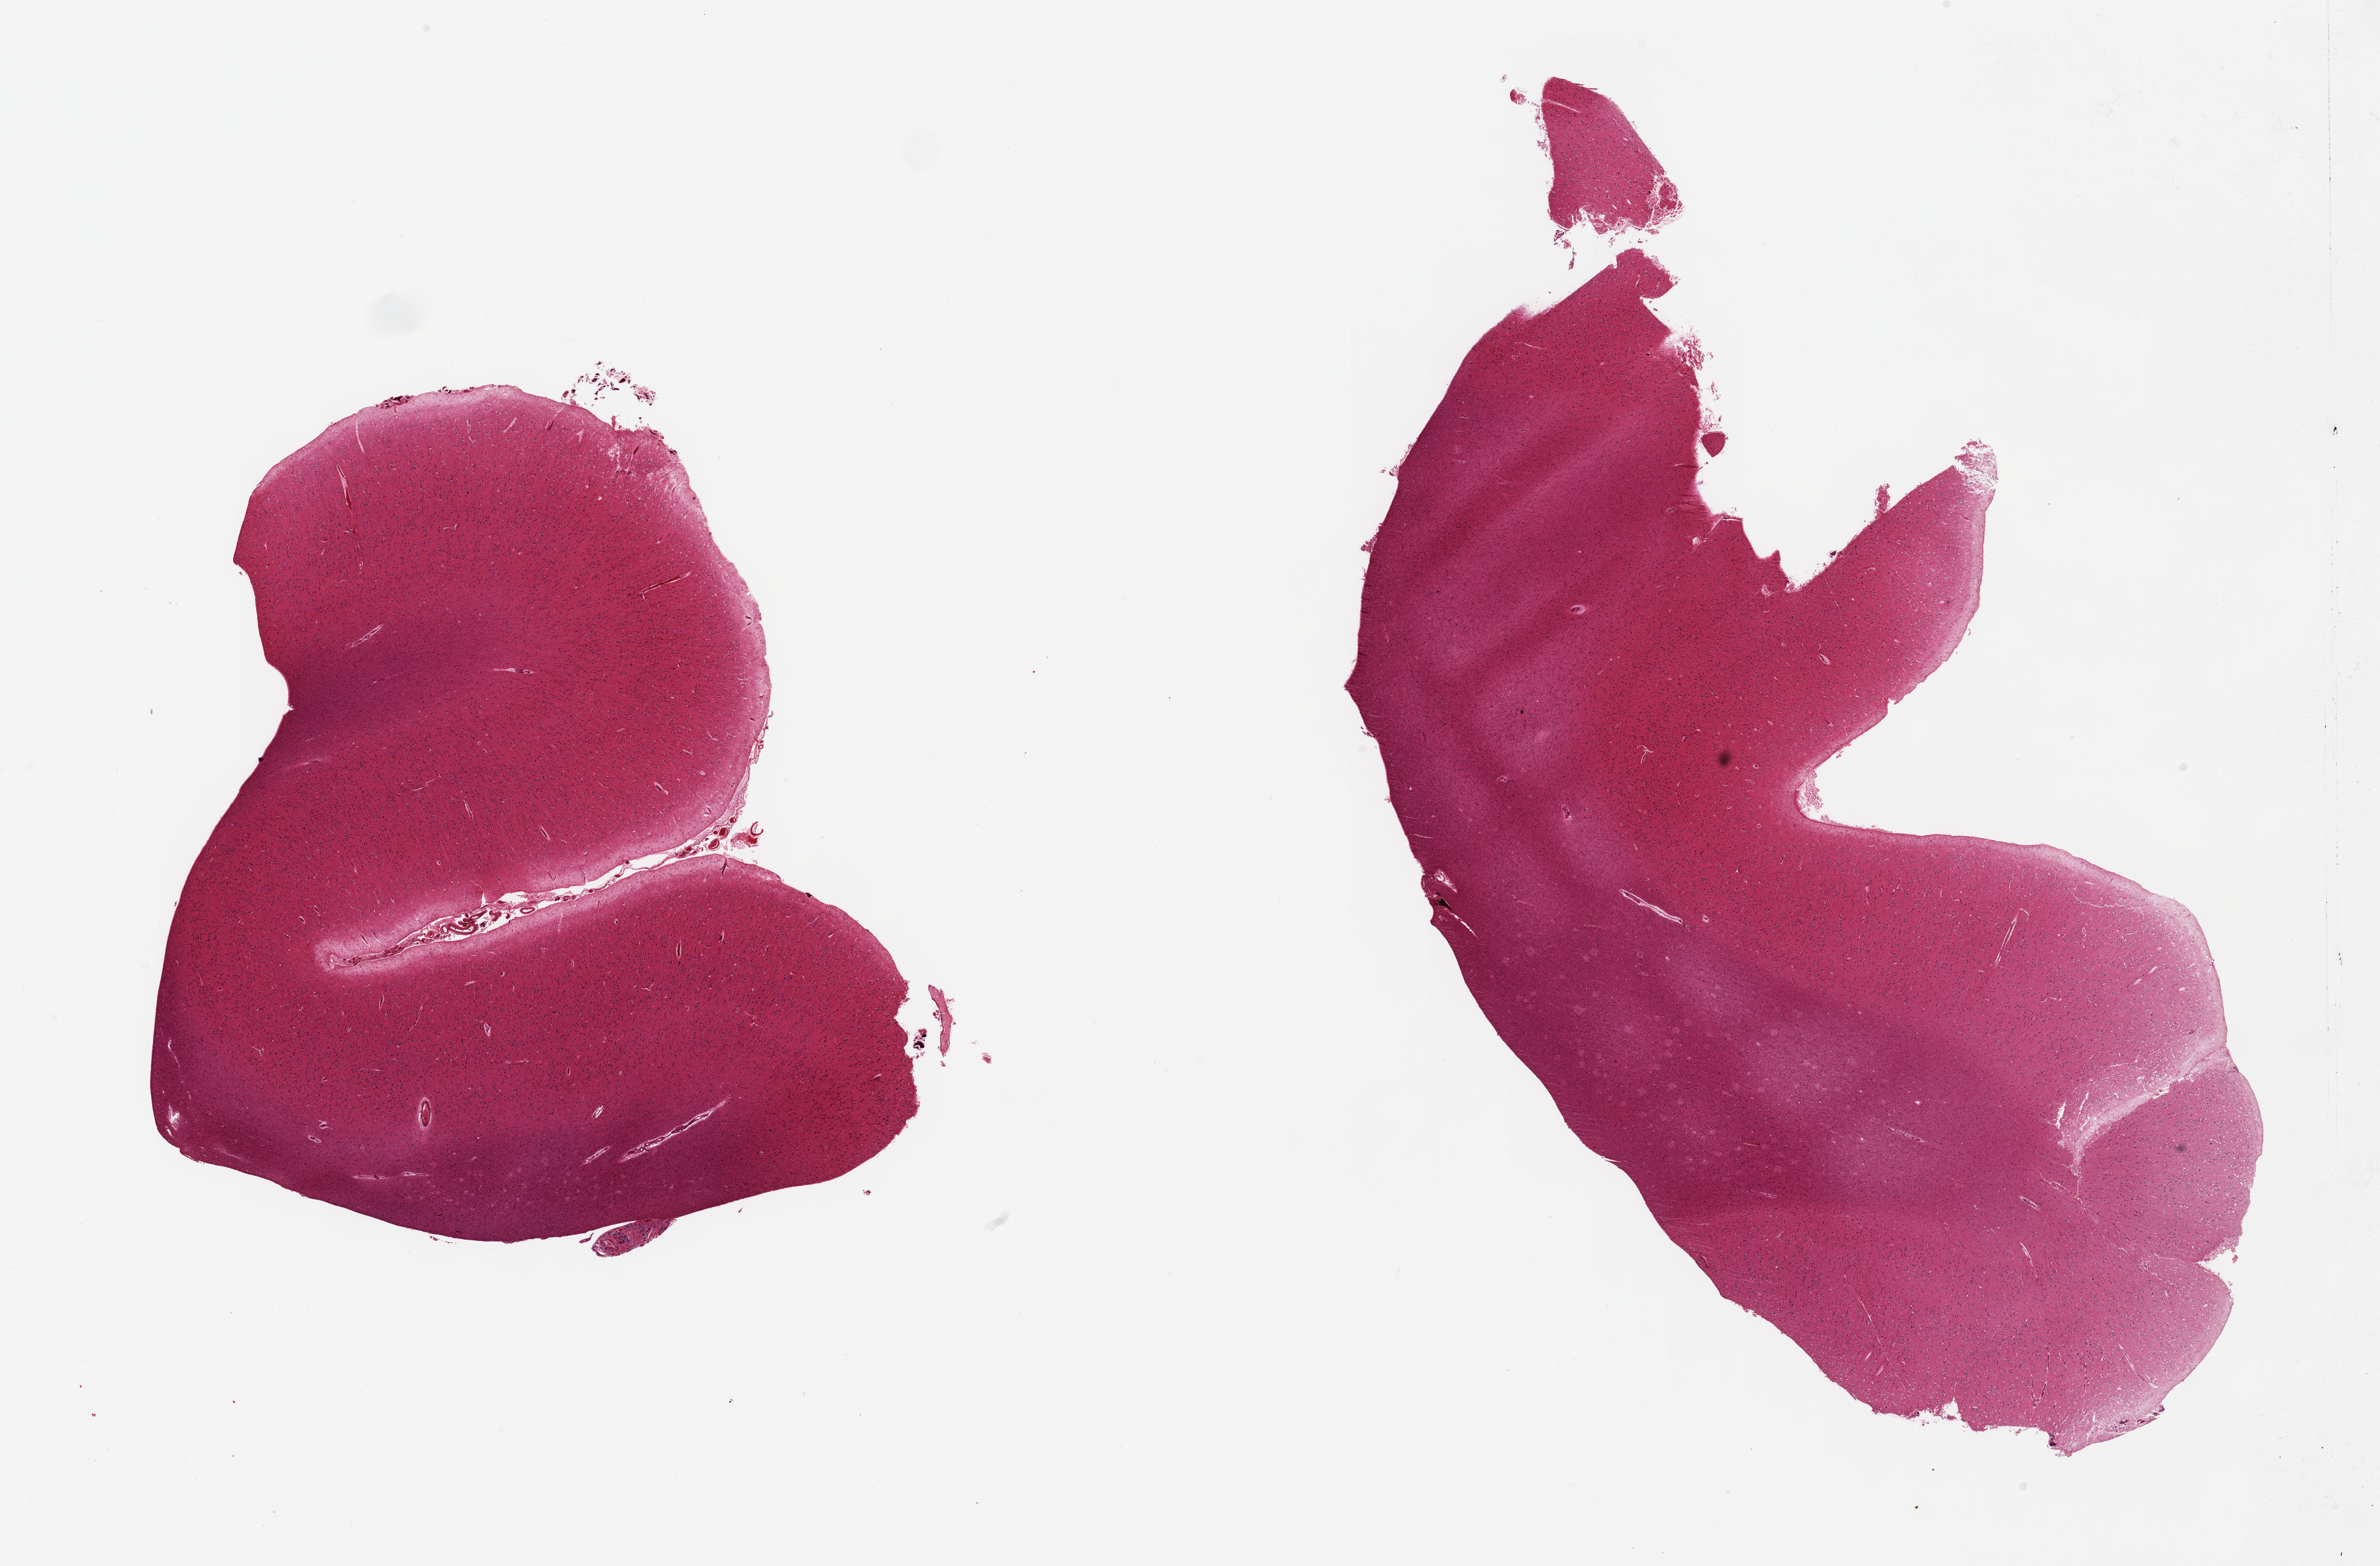
Digitized haematoxylin and eosin-stained section, brightfield — whole scanned area (about 29.5 x 19.4 mm, acquisition: 20x scan) shown as a low-resolution overview, PAXgene-fixed paraffin-embedded (PFPE) section, sampled site (target tissue): cerebral cortex, donor tissue sample. Donor: male.
Review note (as recorded): 2 pieces; oversized.